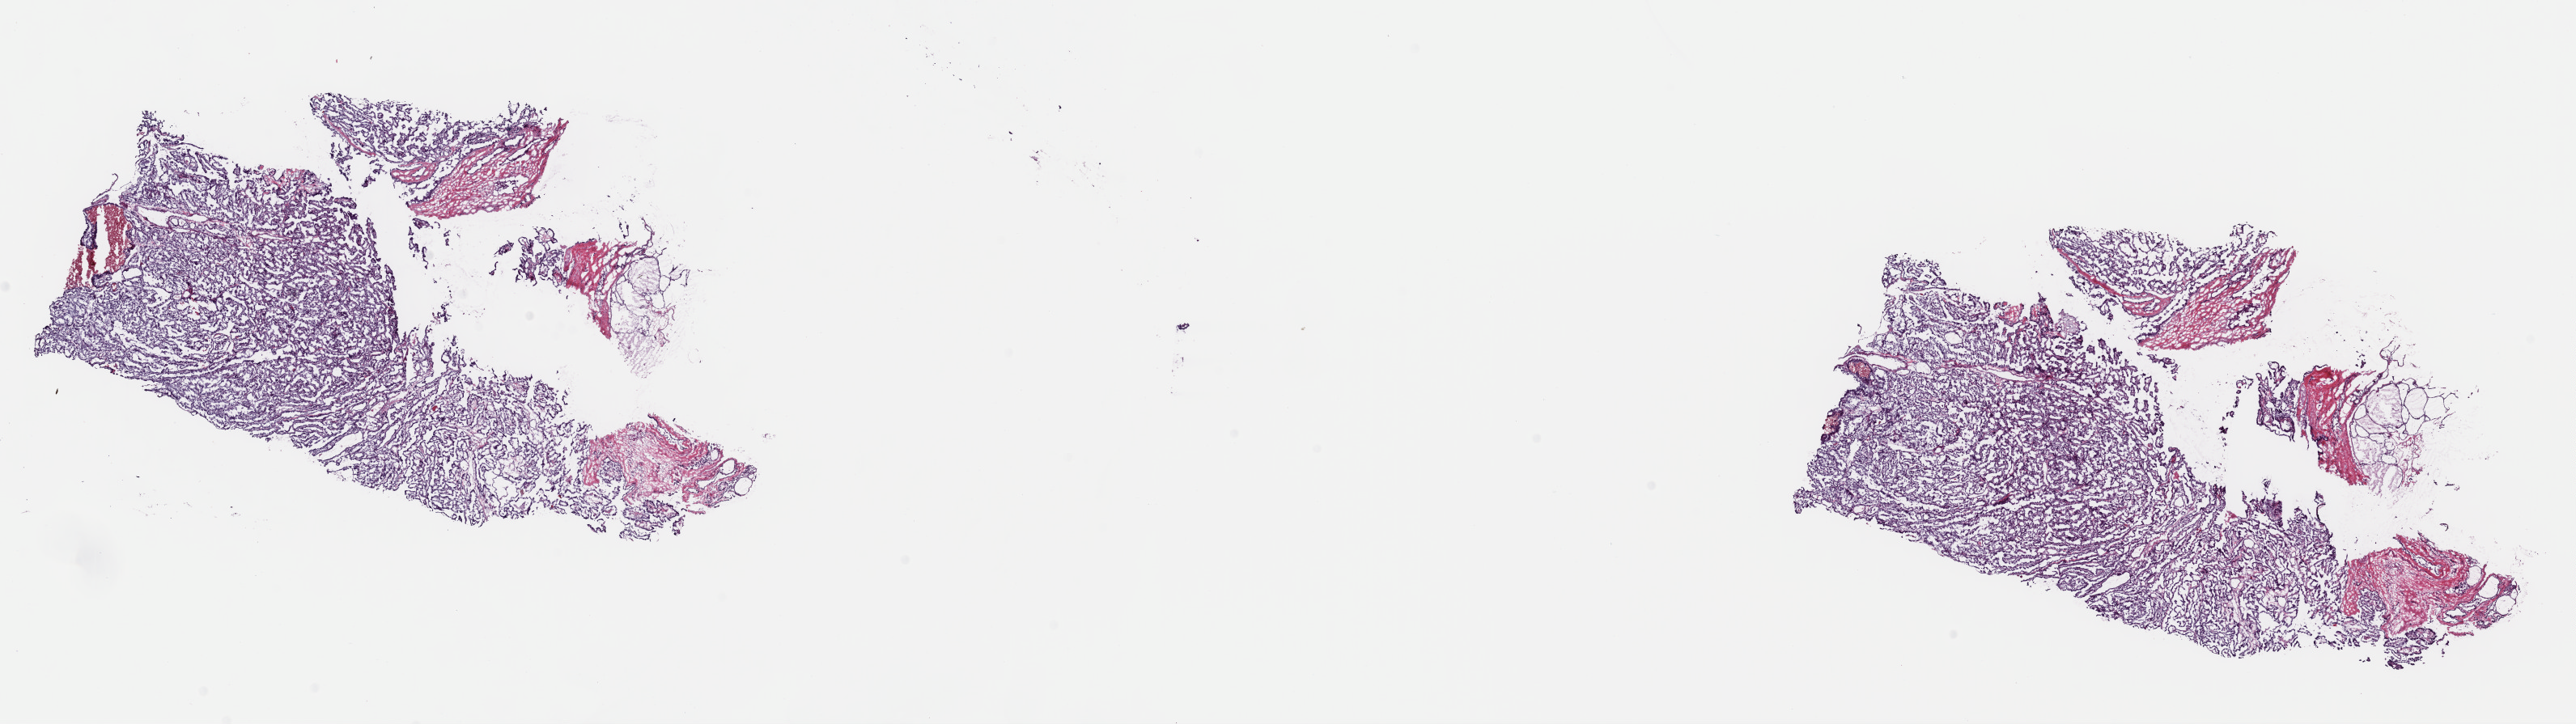
H&E whole-slide image — a low-resolution overview of the entire scanned area, about 25.1 x 7.1 mm; frozen section; sample: primary tumour, thyroid. Patient: female, age at initial diagnosis 46 years. Composition of this section per pathologist review: tumour cells 85%, tumour nuclei 90%, normal cells 5%, stromal cells 10%, necrosis 0%. Inflammatory infiltration, as recorded: lymphocyte infiltration 0%, monocyte infiltration 0%, neutrophil infiltration 0%.
Laterality: right. AJCC pathologic stage: I (6th edition). Pathologic diagnosis: Papillary adenocarcinoma, NOS (thyroid gland).